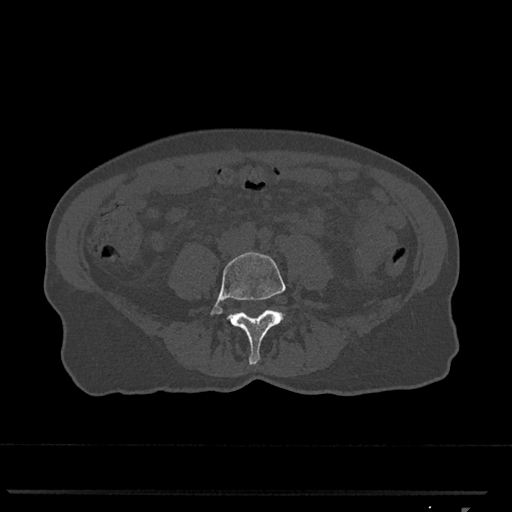
CT including the spine, one axial slice. Position 203 of 793 along the scan axis. Reconstruction kernel Br40s/3. 120 kVp. Bone window (W 1800 / L 400 HU). 0.5 mm slice thickness. 512 × 512 image matrix, field of view 380 × 380 mm. Female patient, age 62 years. From the clinical record (not read from this slice): primary cancer: renal.
Outlined on this slice (semi-automatically segmented with operator editing):
- L4 vertebra: bounding box [x1, y1, x2, y2] px = [211, 252, 286, 365]
- L5 vertebra: [282, 313, 285, 318]